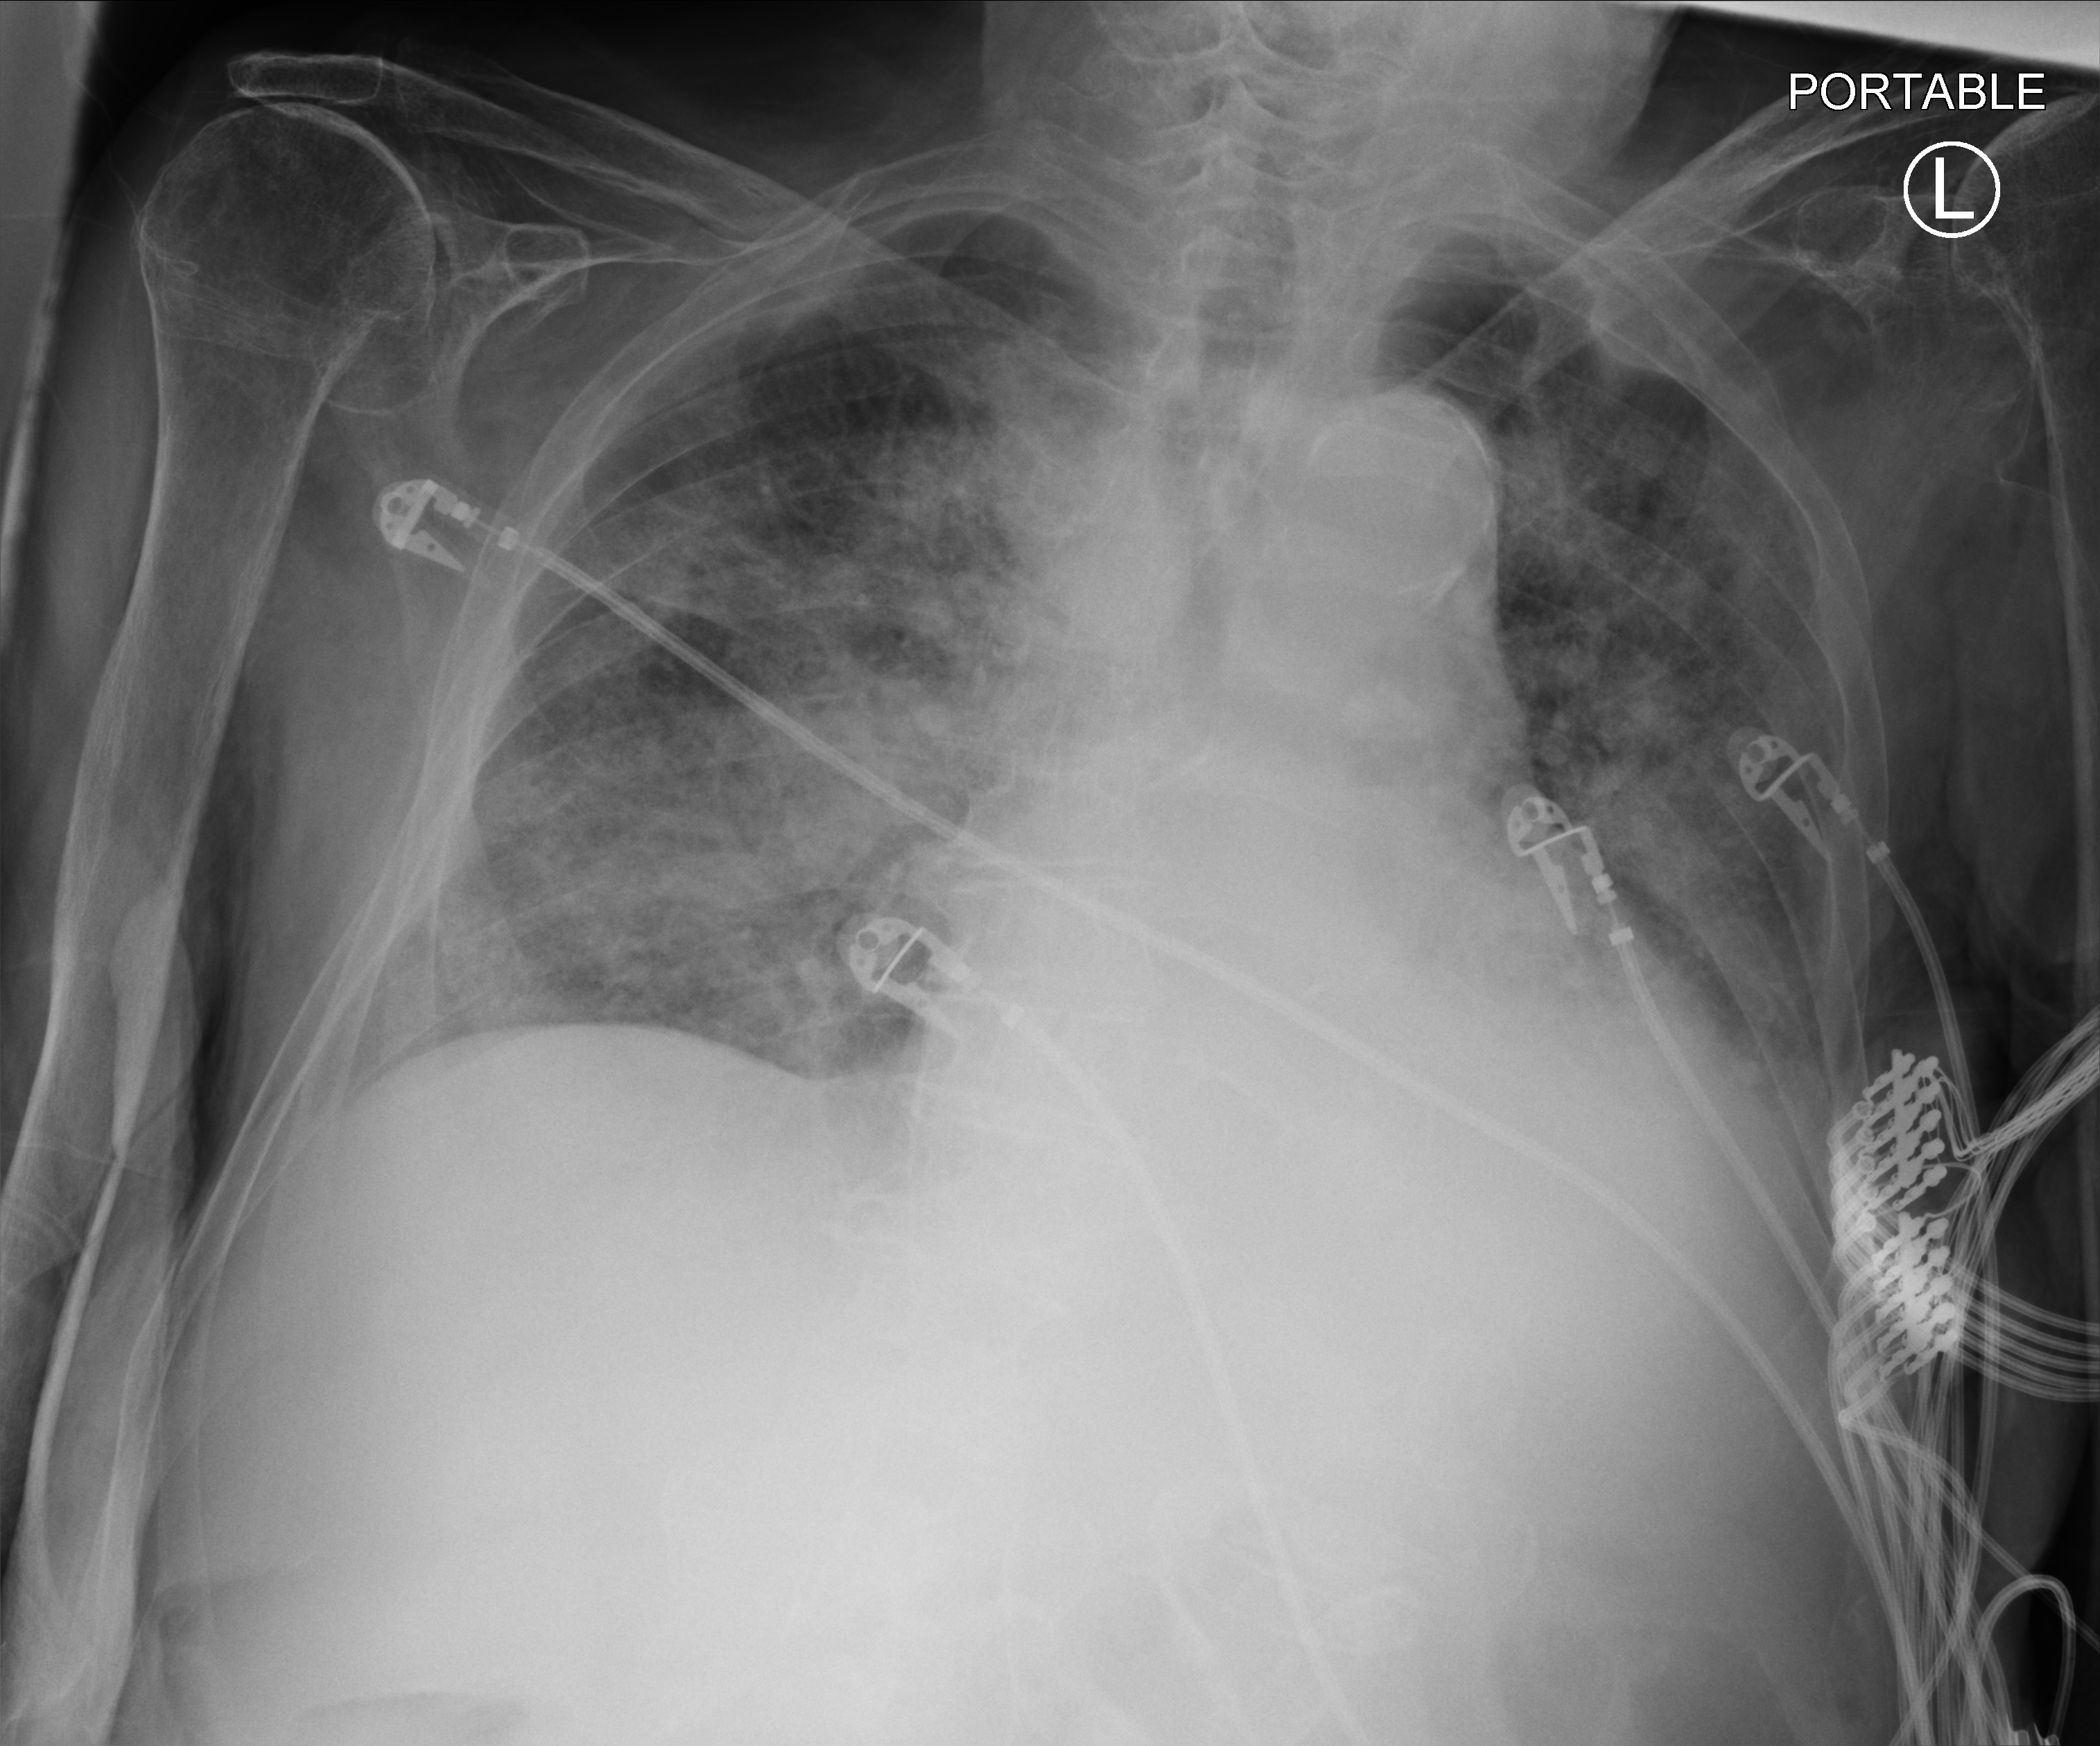
Bedside chest radiograph (computed radiography). Patient hospitalised with COVID-19; male, aged 75–90 years.
Hospital-stay facts (about this admission, not read from this image; timing relative to this image not recorded): admitted to intensive care during this hospital stay: no; mechanically ventilated during this hospital stay: no.